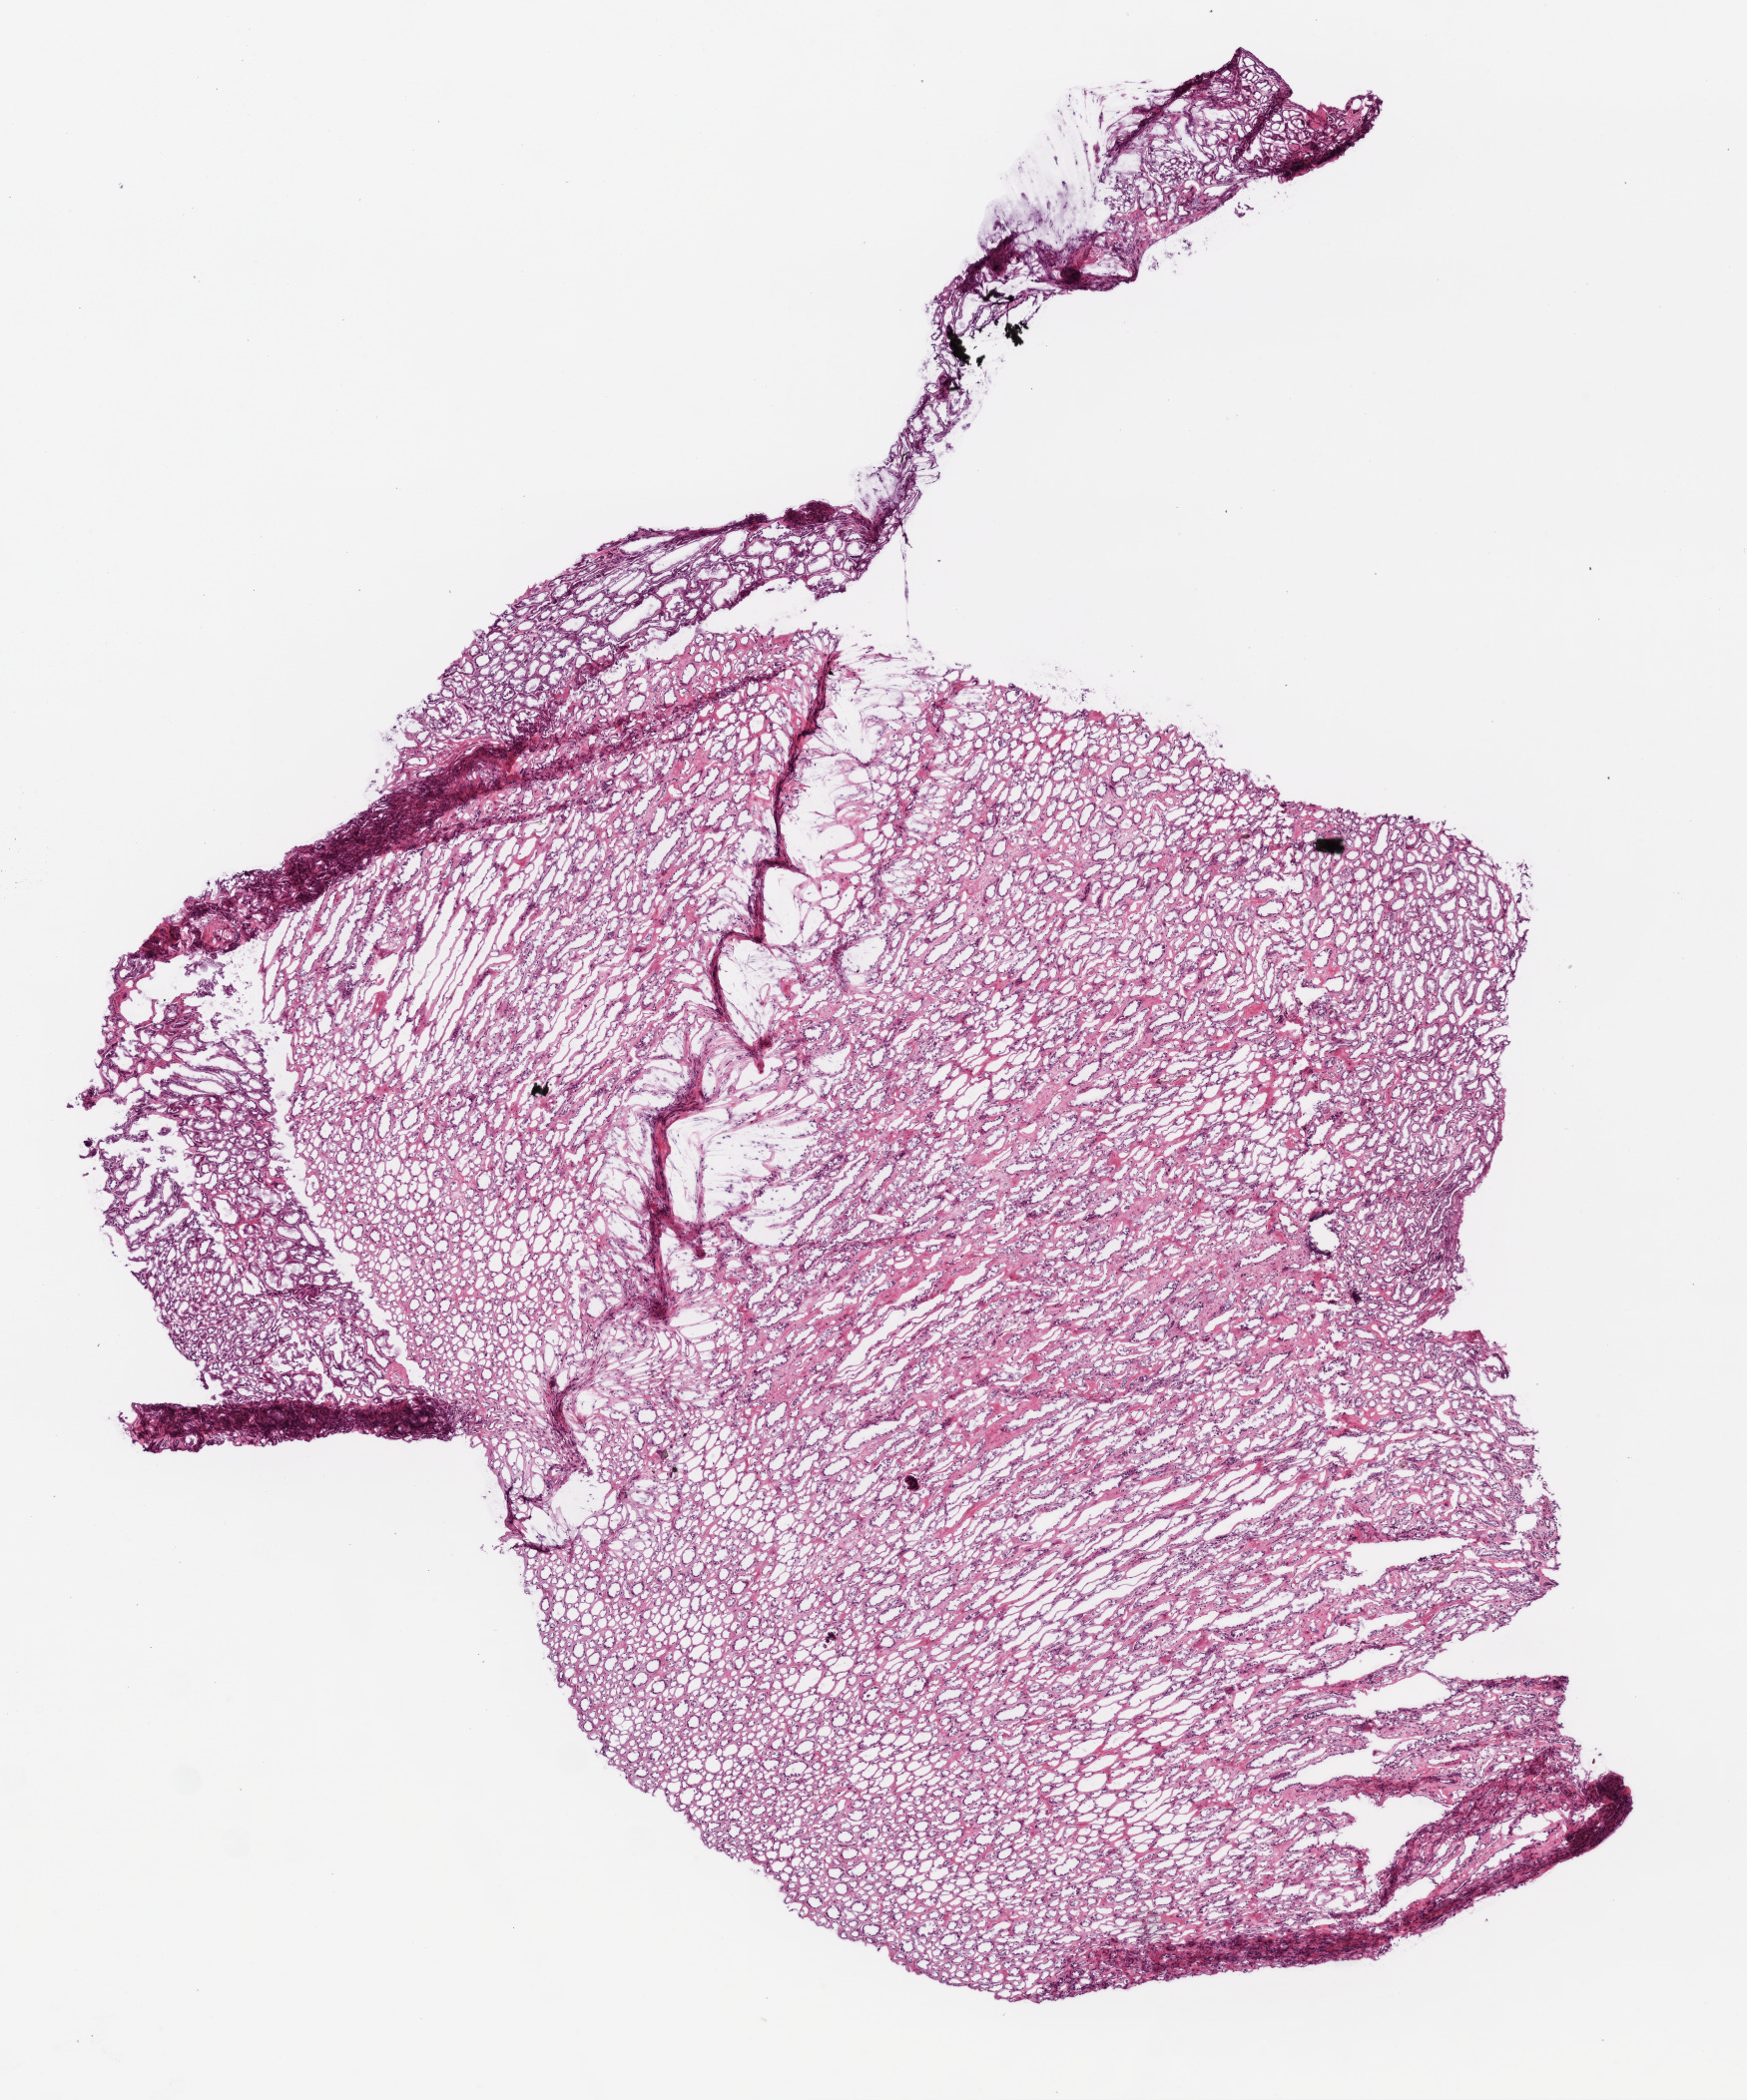
Digitized Hematoxylin and eosin (H&E) stained tissue section (whole slide), whole scanned area (about 7.0 x 8.4 mm, from a 20x scan) shown as a low-resolution overview, frozen section from the top of the tissue portion, kidney, solid tissue normal (non-tumour tissue) sample. Patient: female, age at initial diagnosis 73 years.
• this section: solid tissue normal sample (biorepository sample class)
• patient diagnosis: Clear cell adenocarcinoma, NOS